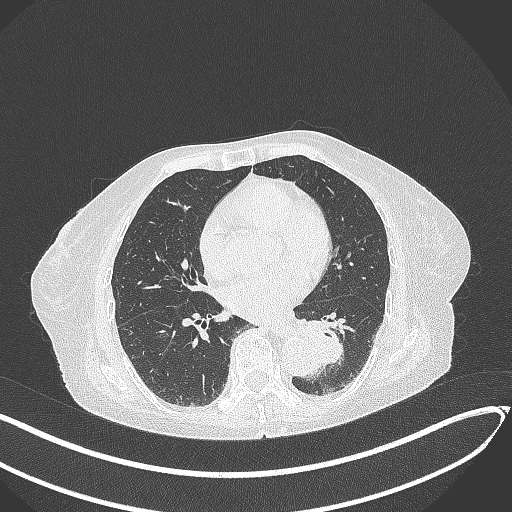
Chest CT, one axial slice. Position 108 of 324 along the scan axis. Reconstruction kernel B70f. Lung window (W 1500 / L -600 HU). 1 mm slice thickness. 512 × 512 image matrix, field of view 400 × 400 mm. Patient: female, 82 years. Case-level facts recorded for this patient, not image findings: clinical TNM (as recorded): T1b N0 M1.
Annotated regions visible in this slice (rectangle marked by the reading radiologist):
- lung tumour (recorded histology: adenocarcinoma): bounding box [x1, y1, x2, y2] px = [294, 314, 350, 368]